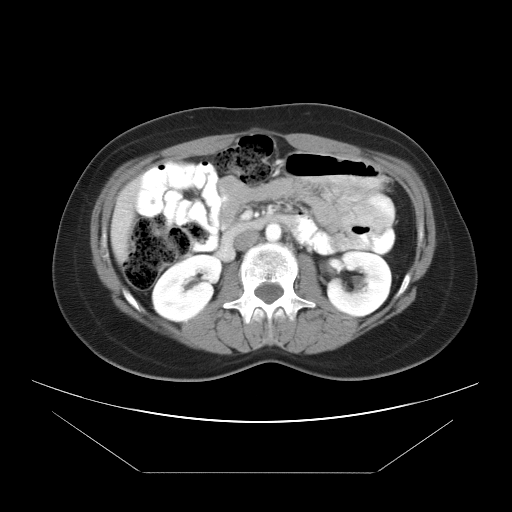
Contrast-enhanced abdominal CT, one axial slice. Position 16 of 34 along the scan axis. Reconstruction kernel STANDARD. Intravenous contrast given. Soft-tissue window (W 400 / L 40 HU). 7.5 mm slice thickness. 512 × 512 image matrix, field of view 410 × 410 mm. Female patient, age 38 years. Case-level facts recorded for this patient, not image findings: diagnosis: colorectal cancer liver metastases, imaged before liver resection; multiple liver metastases: yes; largest metastasis: 3.1 cm; disease in both lobes: no.
Annotated regions visible in this slice (outlined manually by an expert reader):
- liver: bounding box <112,182,142,260> (left, top, right, bottom; pixels)